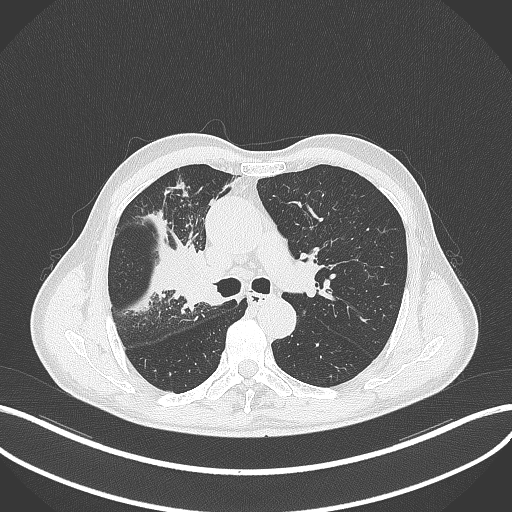
Chest CT, one axial slice. Slice 314 of 490 in the series (ordered by position). Reconstruction kernel B70f. Lung window (W 1500 / L -600 HU). 1 mm slice thickness. 512 × 512 image matrix, field of view 400 × 400 mm. Patient: male, 69 years. From the clinical record (not read from this slice): clinical TNM (as recorded): T2a N0 M0.
Annotated regions visible in this slice (bounding box drawn by a radiologist):
- lung tumour (recorded histology: adenocarcinoma): bounding box (x1, y1, x2, y2) in pixels: (173, 245, 222, 312)